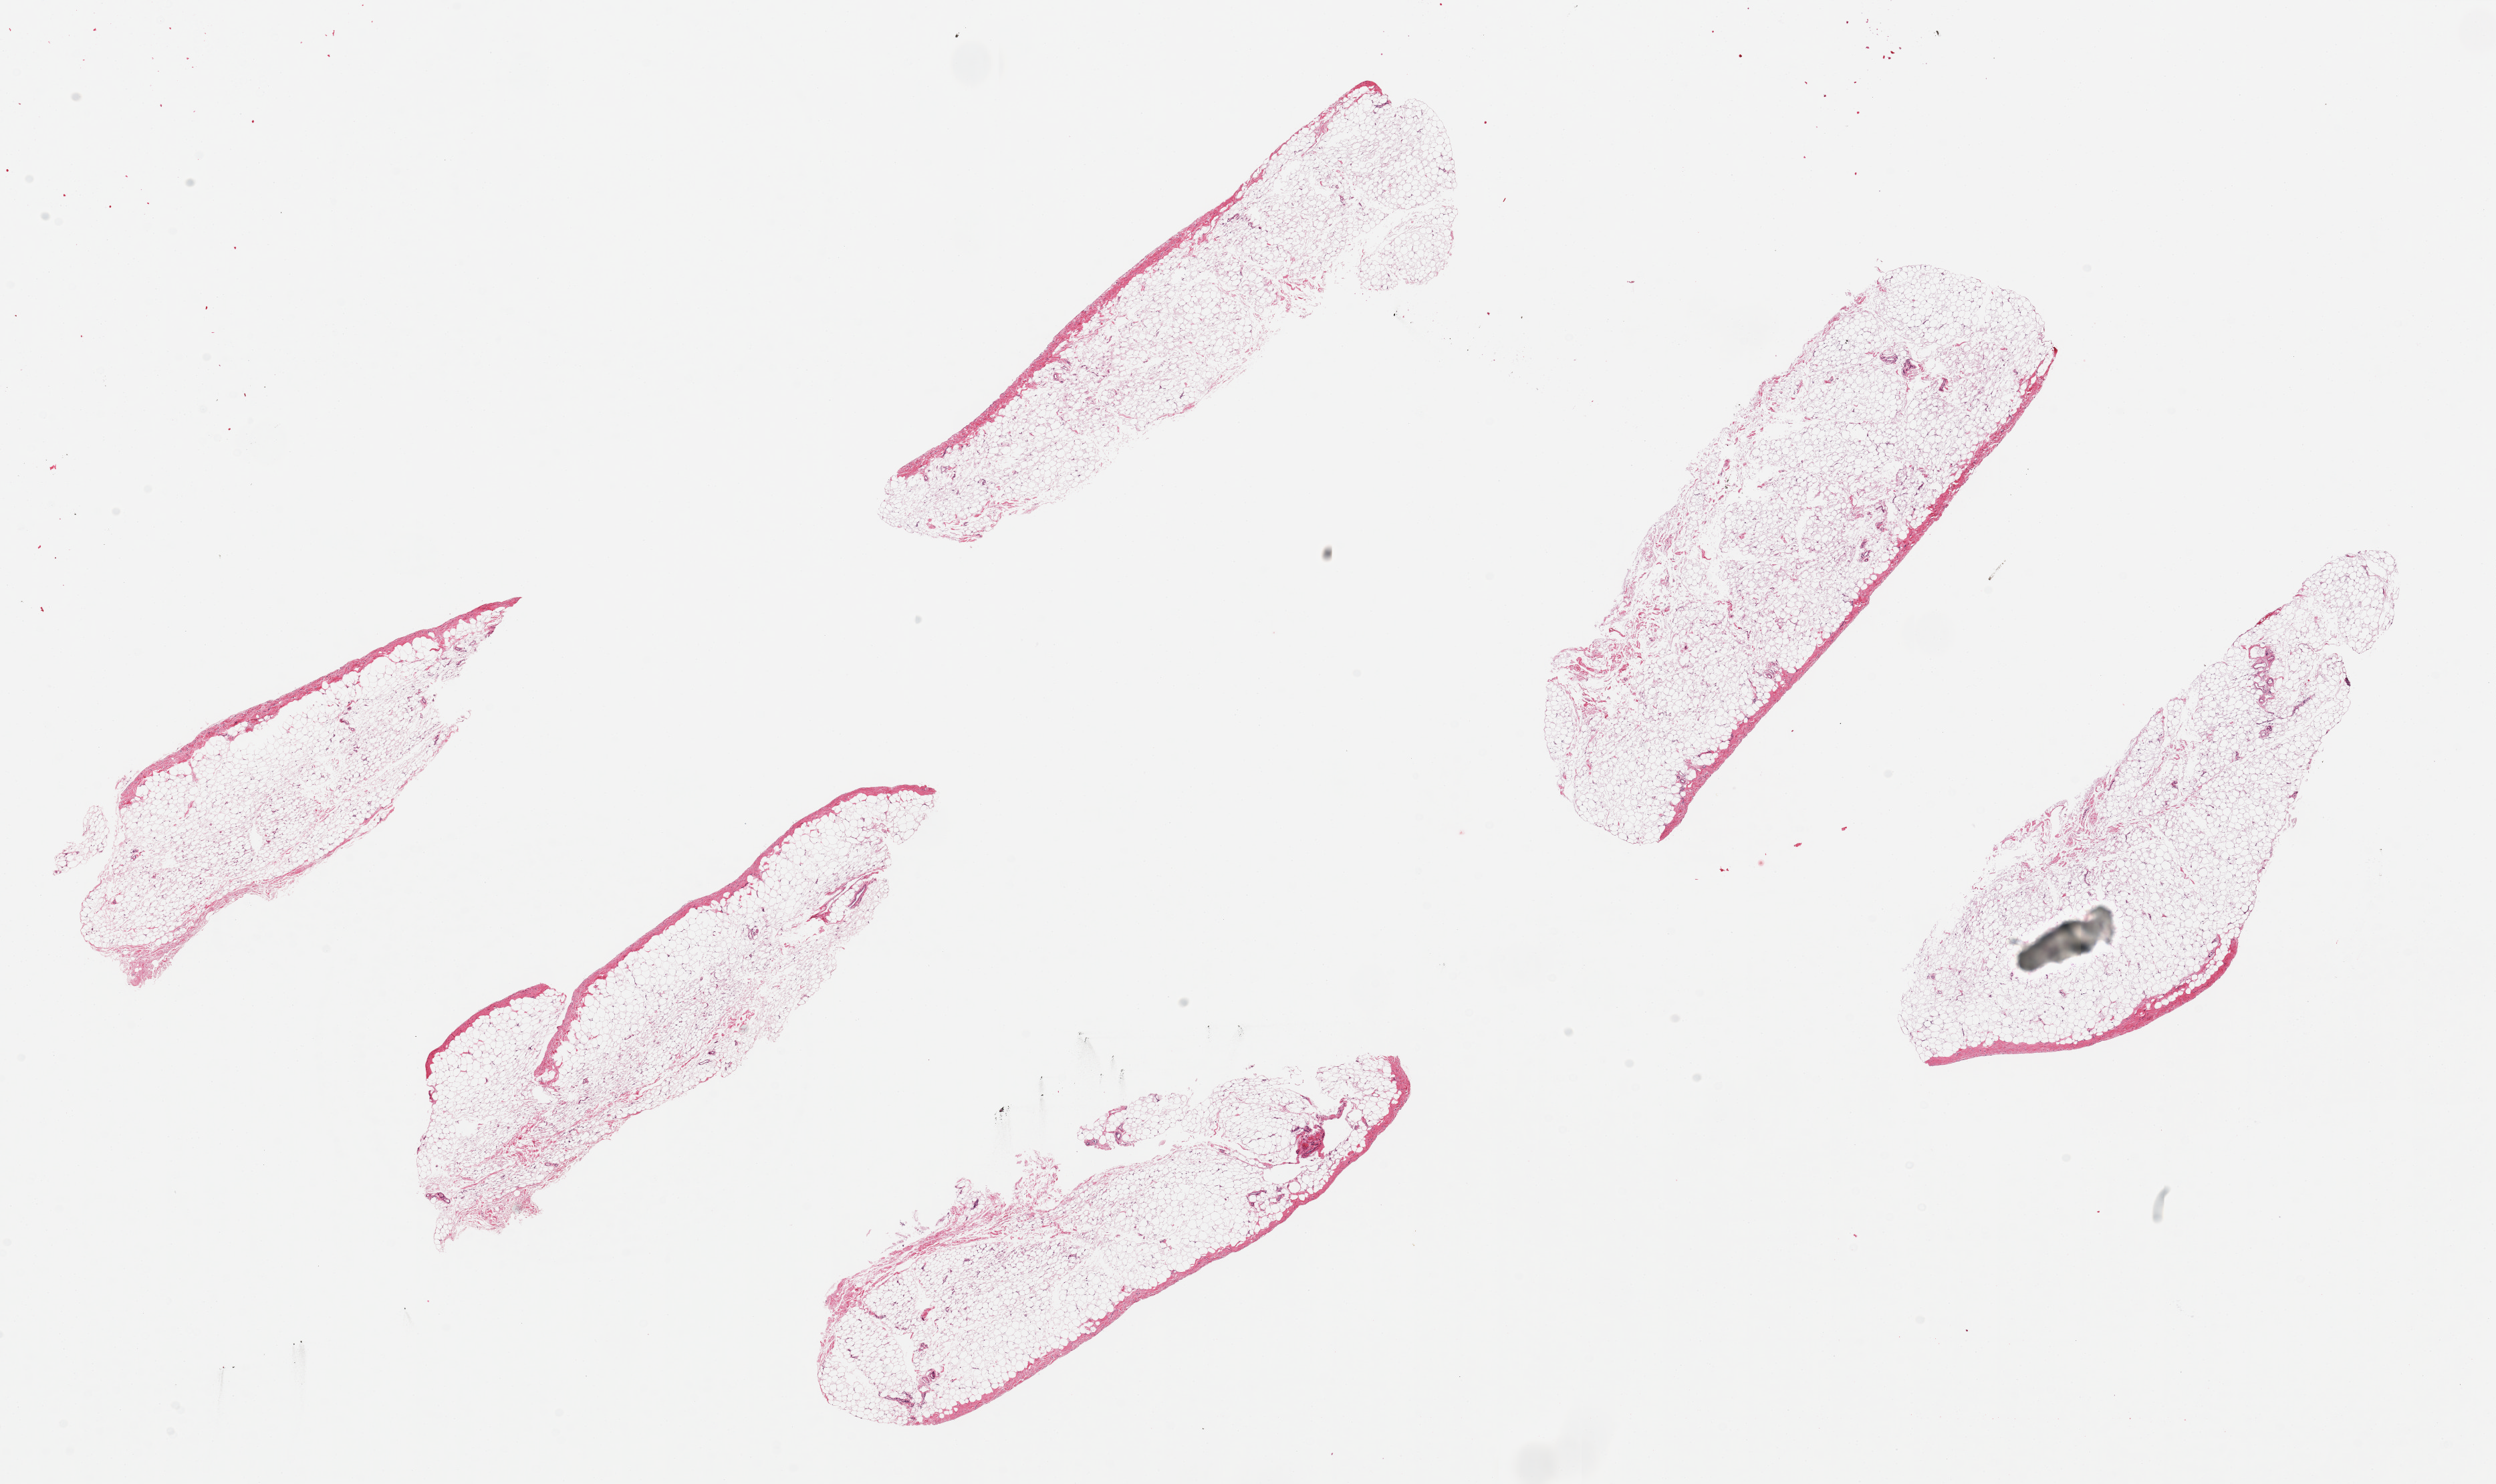
Digitized haematoxylin and eosin-stained section, low-resolution overview of the scanned area, about 29.5 x 17.6 mm (from a 20x scan). Donor sex: female.
- specimen: PAXgene-fixed paraffin-embedded (PFPE) section; section of urinary bladder (target tissue); tissue donor sample